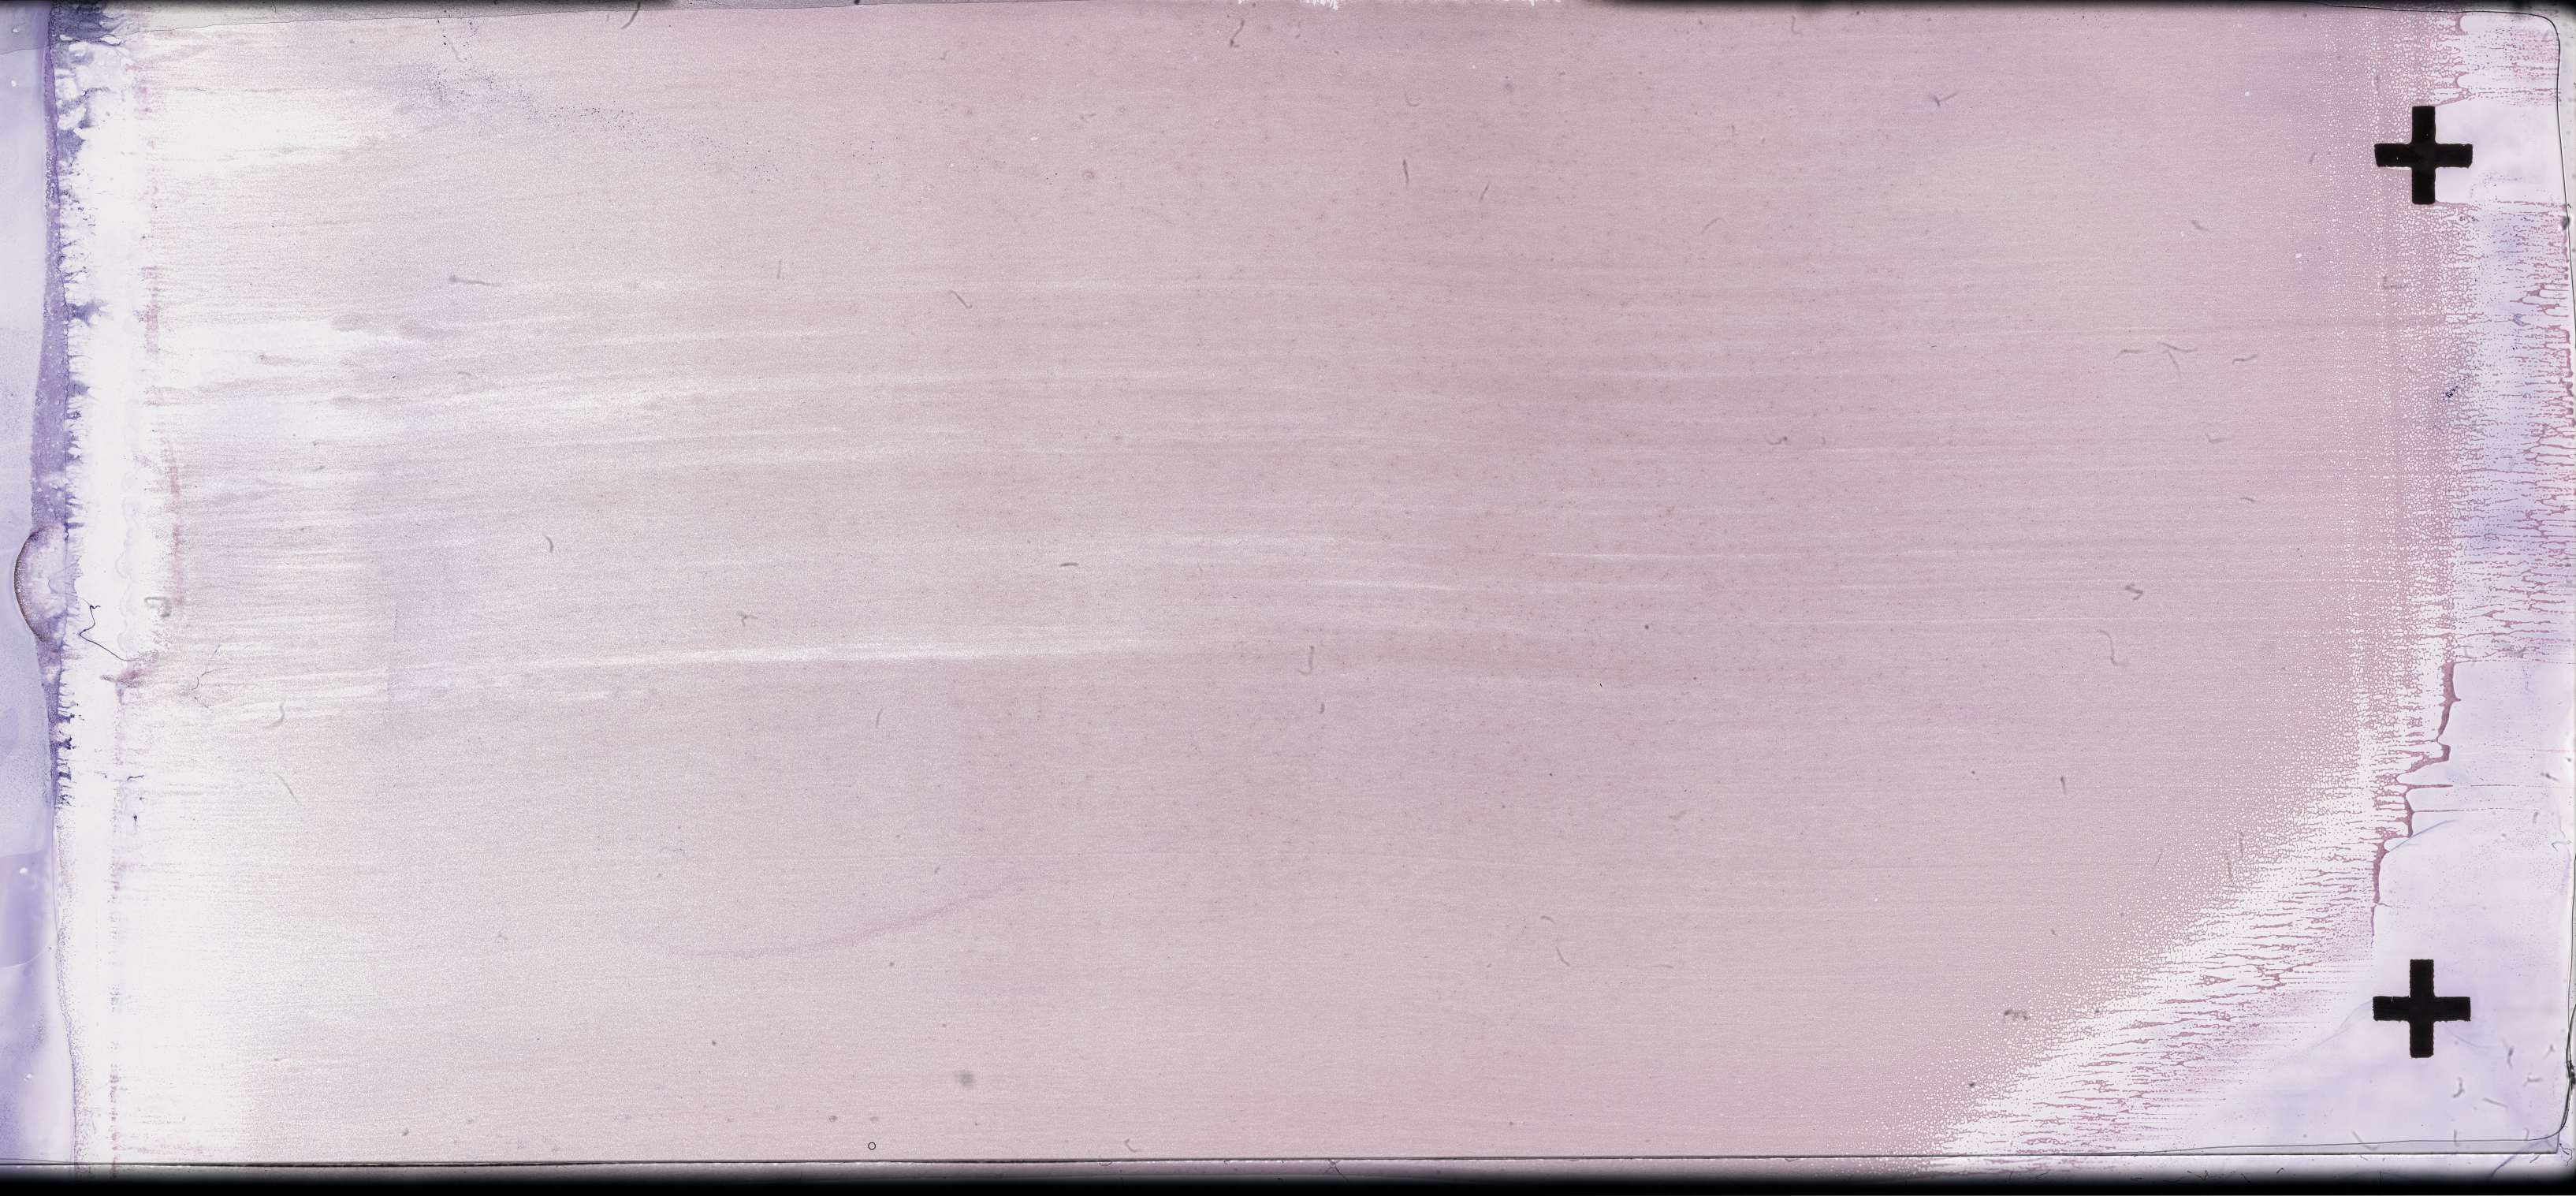
Whole-slide image of a whole blood smear, Wright-Giemsa stain — whole scanned area (about 52.8 x 24.5 mm) shown as a low-resolution overview; smear from an EDTA sample; specimen time point: collected on treatment. Patient sex: female.
From a patient with: Plasma Cell Myeloma.